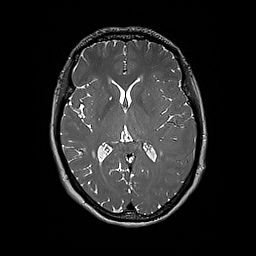
Brain MRI from a brain-tumour surgery series, one axial slice. Position 101 of 192 along the scan axis. 1 mm slice thickness. 256 × 256 image matrix, field of view 250 × 250 mm. From the clinical record (not read from this slice): histopathology: Glioblastoma; WHO grade: 4; IDH mutation: no.
Annotated regions visible in this slice (outlined manually by an expert reader):
- tumour: bounding box [x1, y1, x2, y2] px = [182, 161, 186, 167]